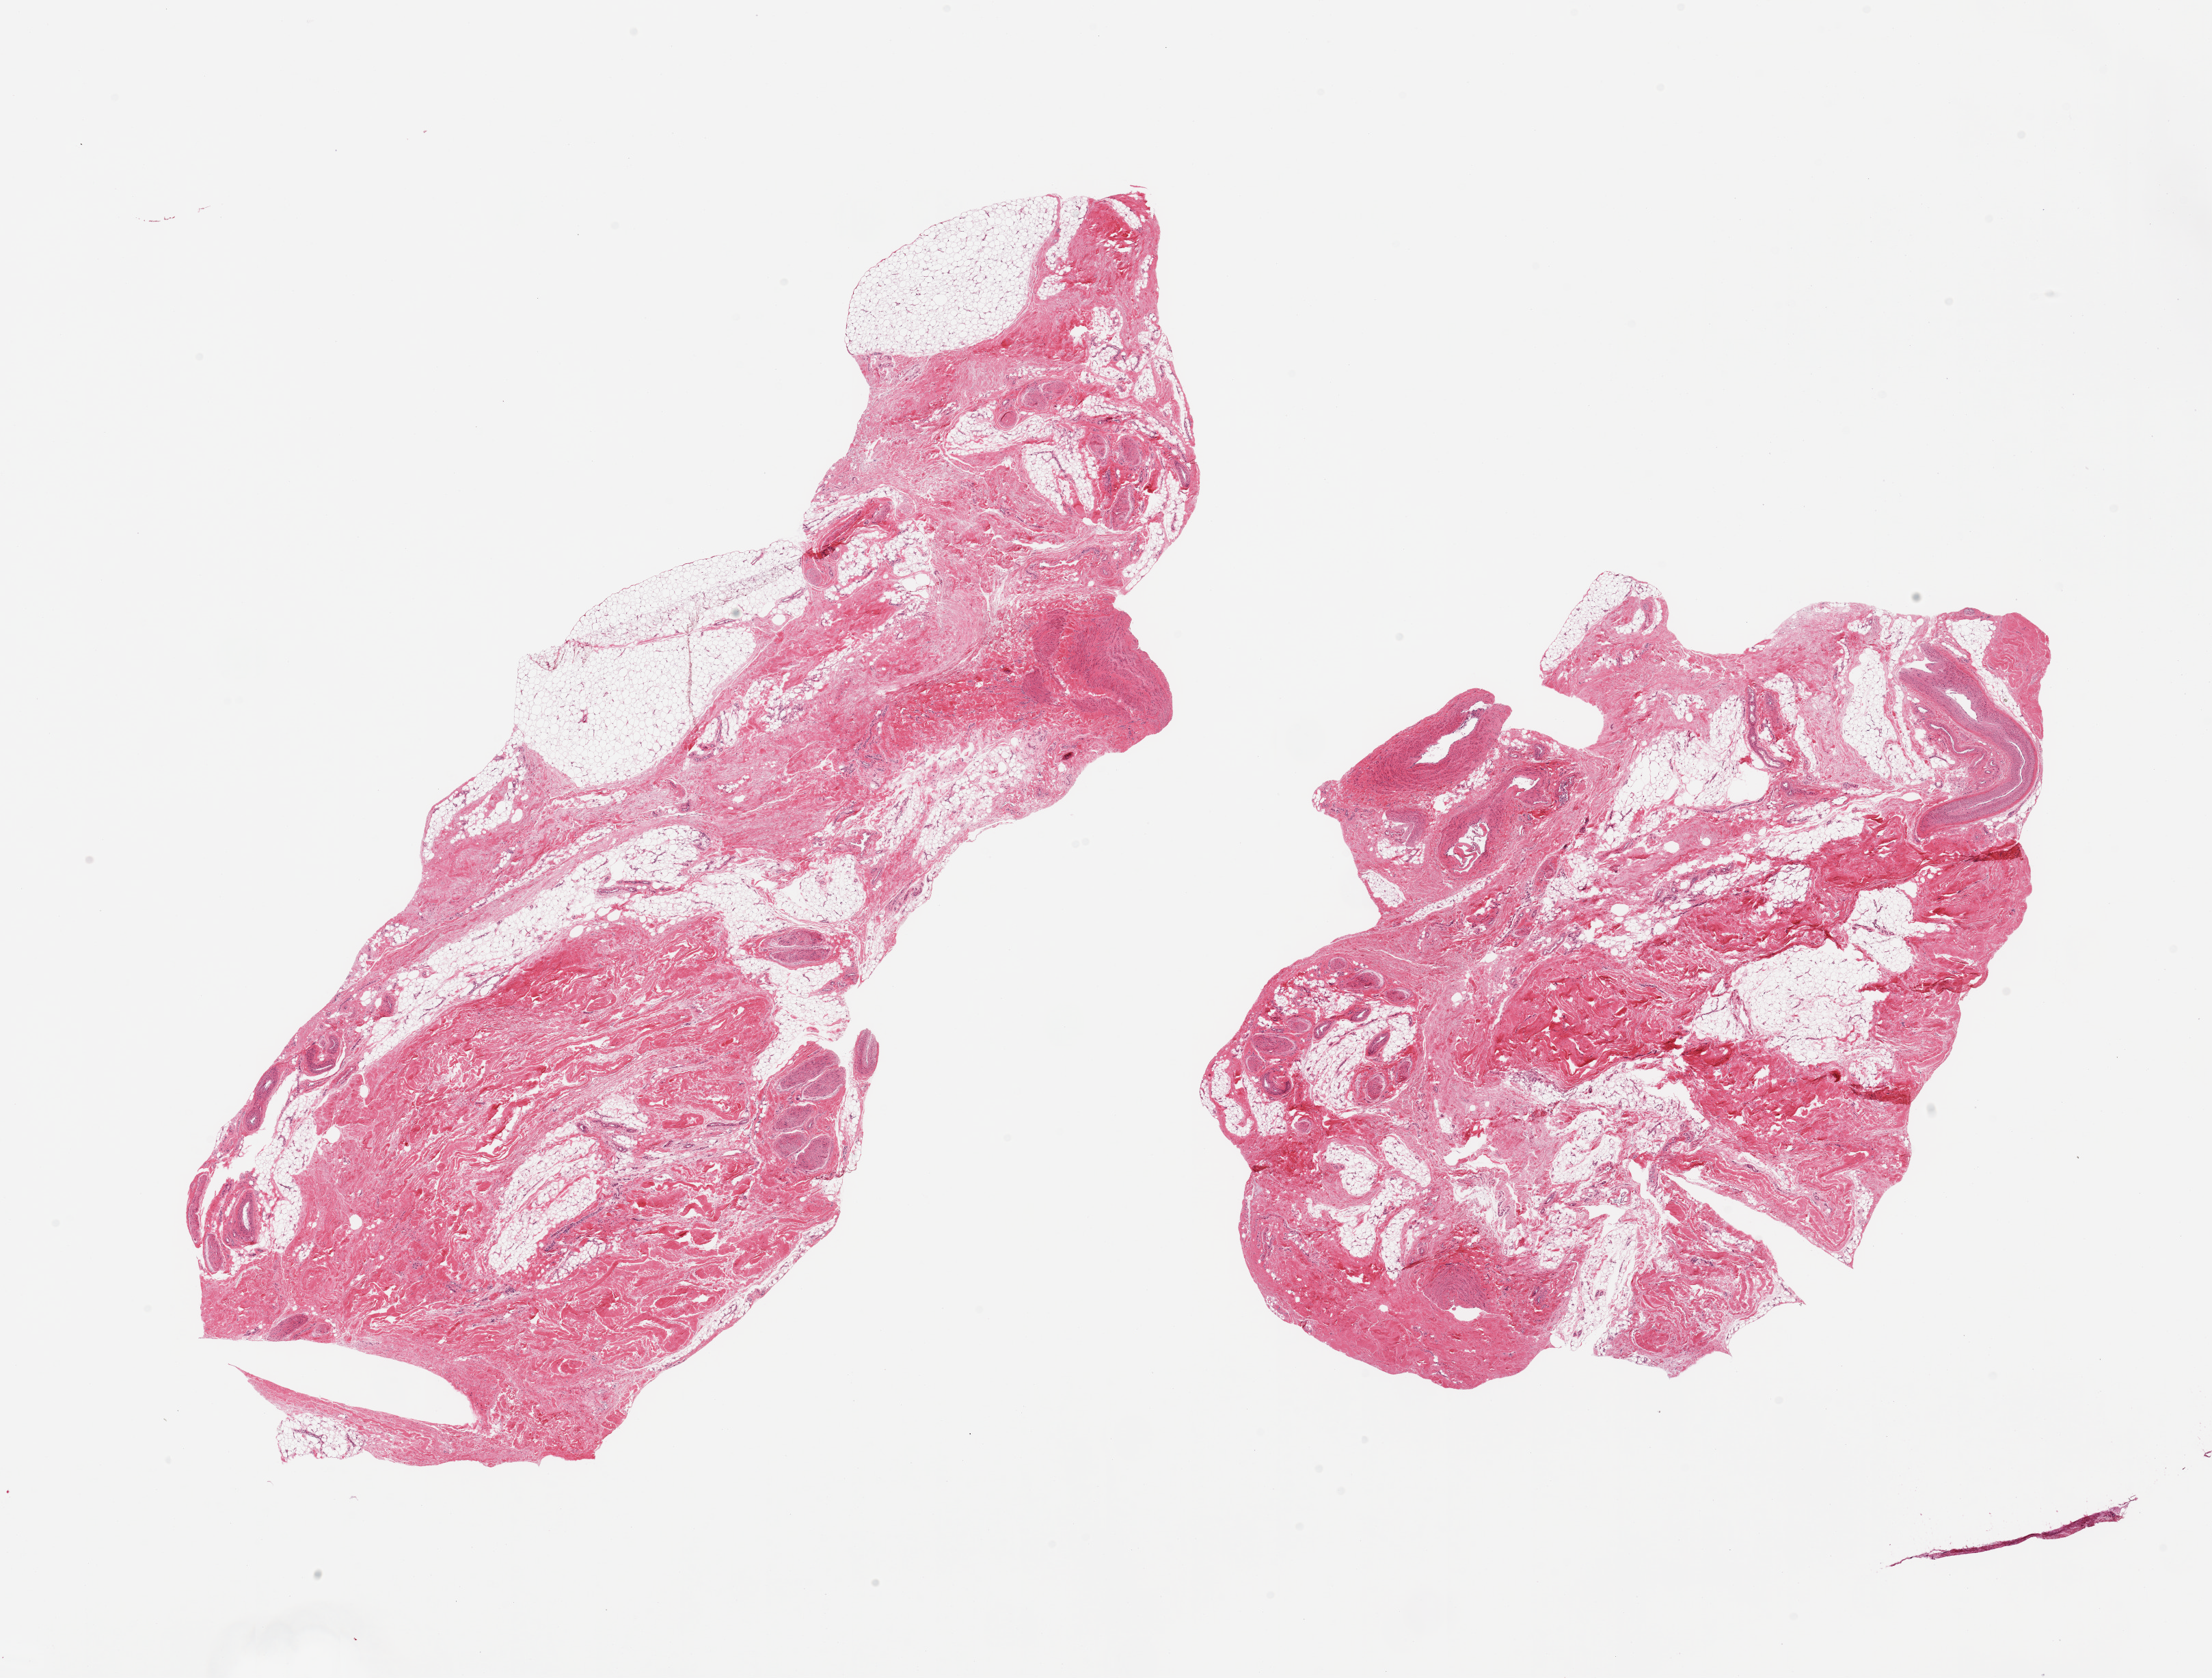
Whole-slide image, haematoxylin and eosin stain — shown as a low-resolution overview of the whole scanned area (about 25.6 x 19.4 mm, from a 20x scan), PAXgene-fixed paraffin-embedded (PFPE) section, sampled site (target tissue): adipose tissue, donor tissue sample. Donor sex: male.
Pathologist's review note for this sample: 2 pieces, ~60% fascia.